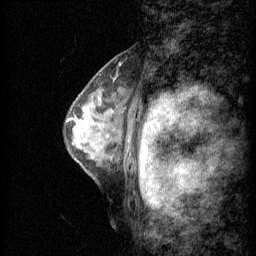
Breast MRI (dynamic contrast-enhanced), one sagittal slice; slice 42 of 60 in the series (ordered by position); 3 images stored at this slice position (order not interpretable as contrast timing); 1.5 T; TE 4.2 ms, TR 11 ms; 1.5 mm slice thickness; 256 × 256 image matrix, field of view 200 × 200 mm. Patient: female, 48 years.
Structures marked on this image (semi-automatic segmentation, software-assisted and operator-edited):
- analysis volume of interest (the breast-tissue region the enhancement analysis was run in; not a lesion): box from (x=65, y=76) to (x=140, y=143) px
- tumour enhancement mask (voxels above the 70 % enhancement threshold inside the analysis volume of interest): (x=67, y=118)–(x=72, y=121)